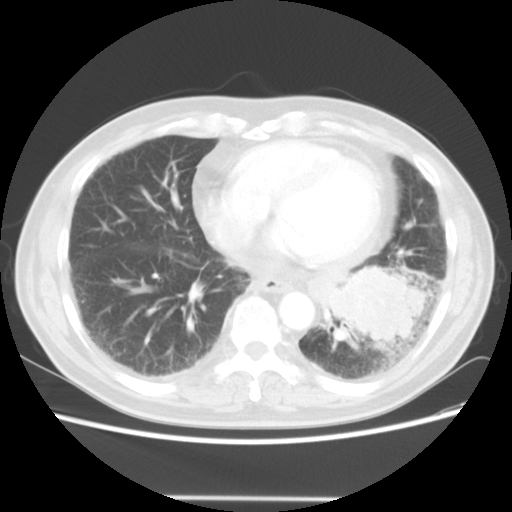
Chest CT, one axial slice. Slice 17 of 56 in the series (ordered by position). Reconstruction kernel STANDARD. 140 kVp. Lung window (W 1500 / L -600 HU). 5 mm slice thickness. 512 × 512 image matrix, field of view 360 × 360 mm. Patient: male, 66 years. From the clinical record (not read from this slice): clinical TNM (as recorded): T4 N3 M0; histopathological grade: G3.
Structures marked on this image (bounding box drawn by a radiologist):
- lung tumour (recorded histology: small cell carcinoma): box from (x=331, y=253) to (x=428, y=350) px